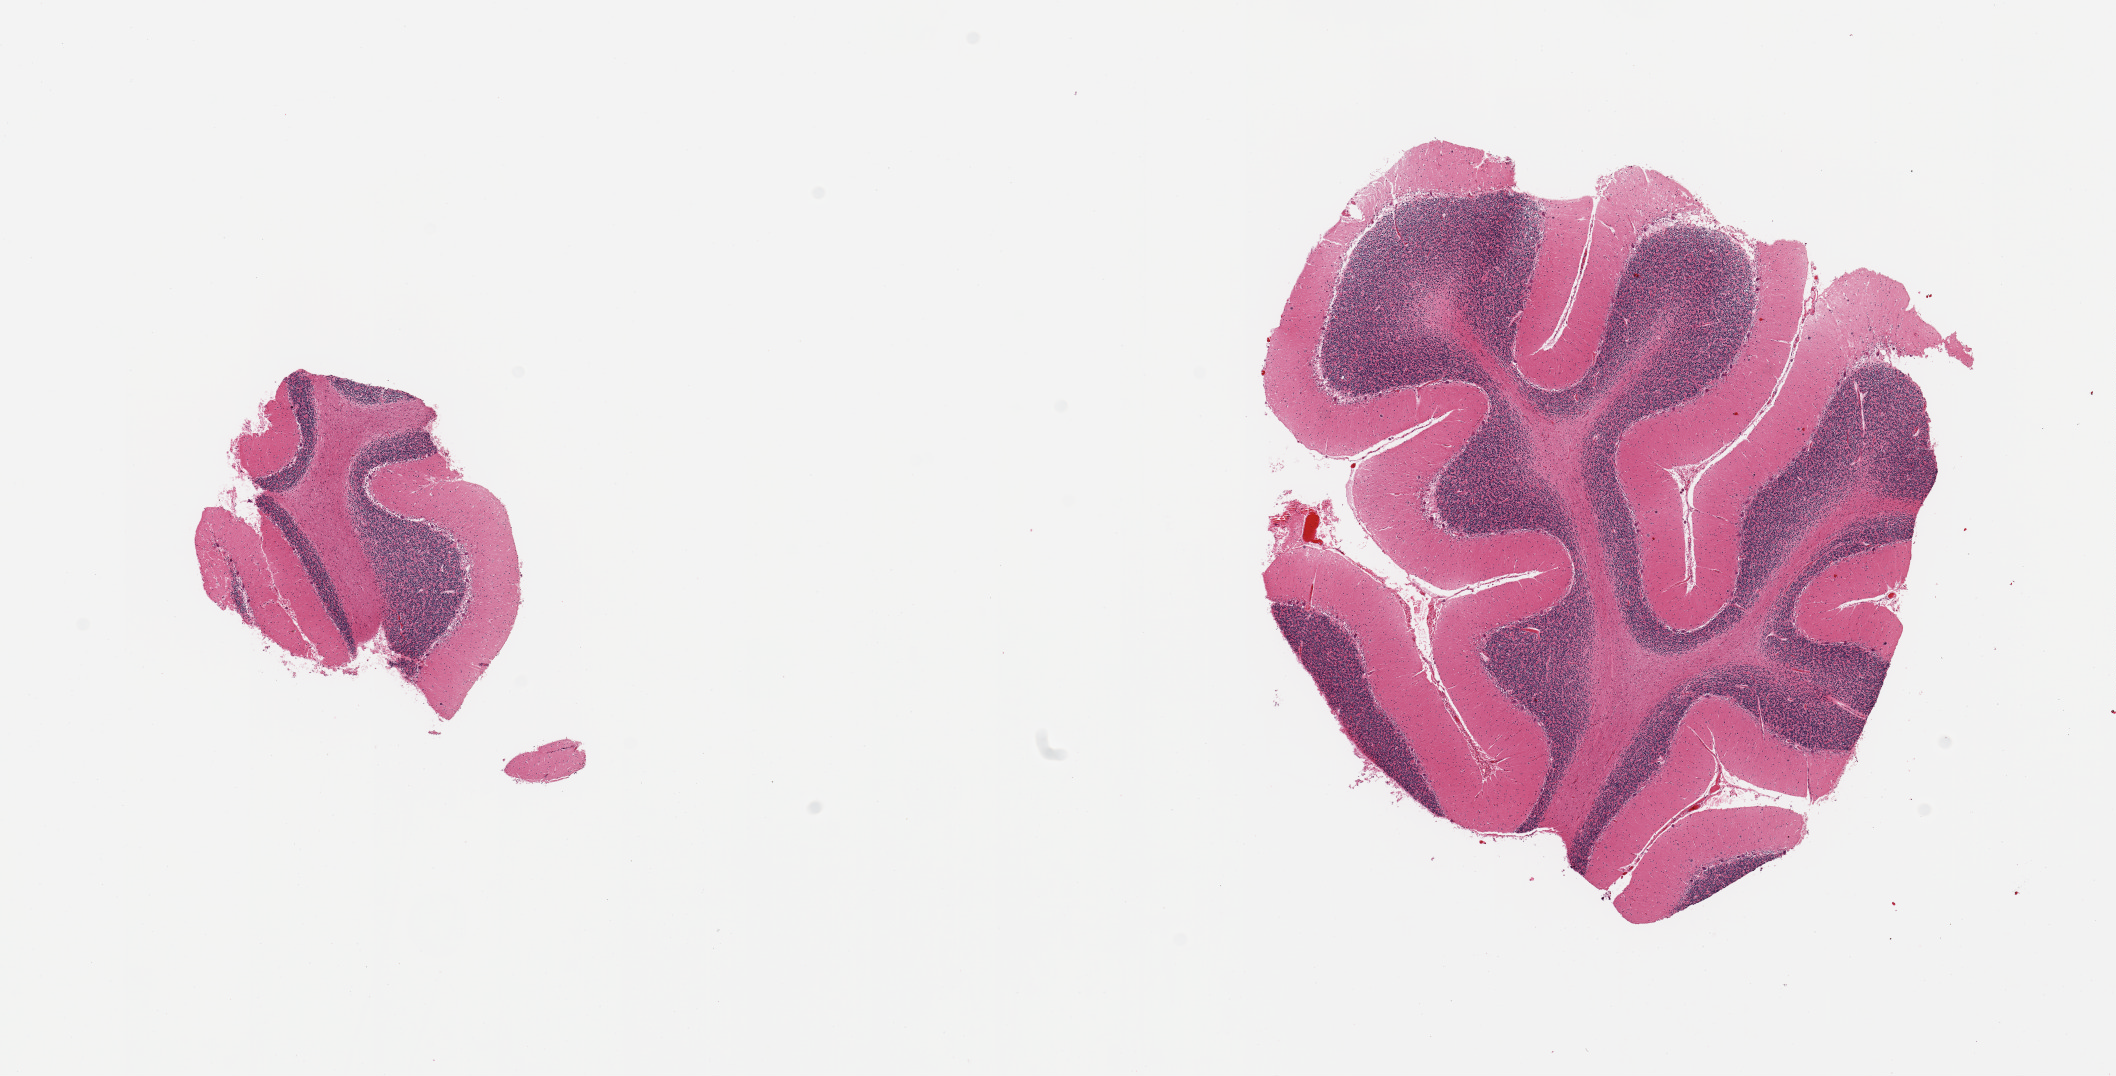
Digitized hematoxylin and eosin (H&E)-stained section — whole scanned area (about 16.7 x 8.5 mm, from a 20x scan) shown as a low-resolution overview, PAXgene-fixed, paraffin-embedded tissue, target tissue: cerebellum, tissue donor sample. Male donor.
Reviewer comment on this tissue sample: 2 pieces; Purkinje cells well visualized.